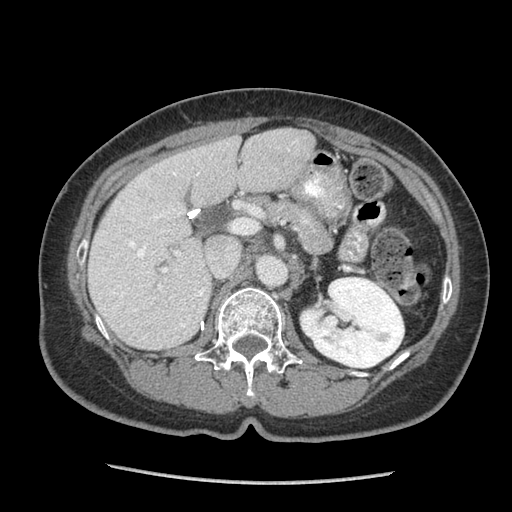
Contrast-enhanced abdominal CT (liver protocol), one axial slice. Reconstruction kernel STANDARD. 140 kVp. Soft-tissue window (W 400 / L 40 HU). 512 × 512 image matrix, field of view 340 × 340 mm. From the clinical record (not read from this slice): diagnosis: hepatocellular carcinoma (patient treated with transarterial chemoembolisation; whether this scan precedes or follows treatment is not stated here); TNM stage (as recorded): Stage-I; Child-Pugh class: A; tumour differentiation: moderately differentiated; tumour nodularity: uninodular.
Structures marked on this image (semi-automatic segmentation, software-assisted and operator-edited):
- liver parenchyma outside the tumour (the mass and vessels are separate outlines, so this box may not span the whole liver): bounding box [x1, y1, x2, y2] px = [88, 128, 314, 350]
- liver vessels: [111, 172, 205, 327]